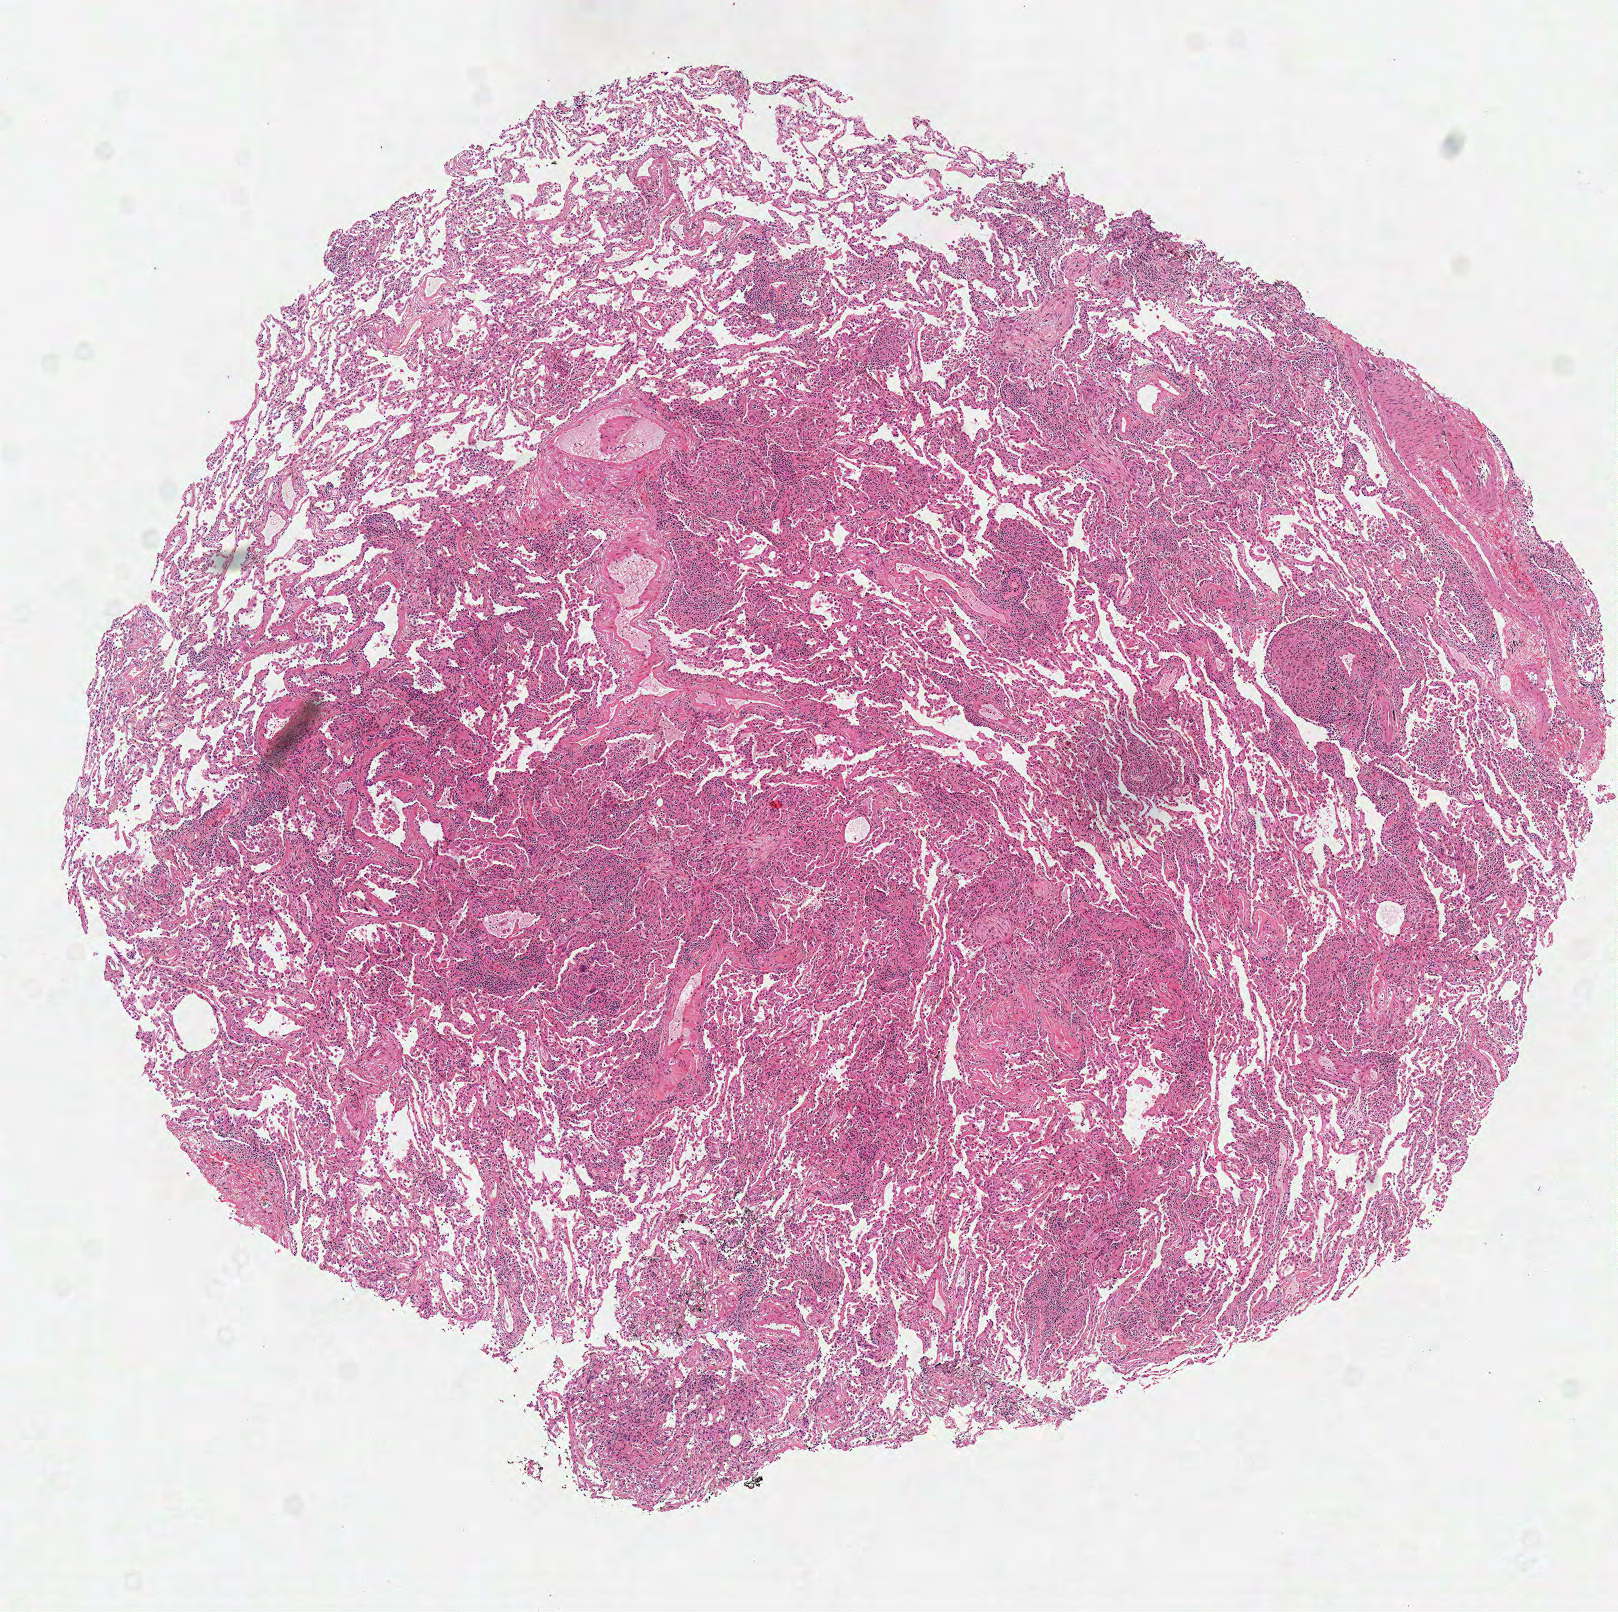
Hematoxylin and eosin (H&E) stained whole-slide image, whole scanned area (about 6.4 x 6.3 mm, acquisition: 40x scan) shown as a low-resolution overview. Frozen section from the top of the tissue portion. Solid tissue normal (non-tumour tissue) sample from the lung. Male, age 60 years at initial diagnosis. Infiltration values recorded for this section: lymphocyte infiltration 20%, monocyte infiltration 40%, neutrophil infiltration 0%.
This section: solid tissue normal (non-tumour) sample from the same patient. Patient diagnosis: Adenocarcinoma, NOS (lower lobe, lung).